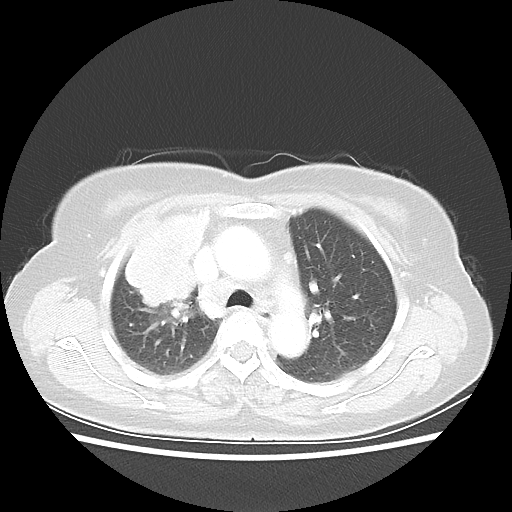
Chest CT, one axial slice; position 37 of 55 along the scan axis; 80 kVp; lung window (W 1500 / L -600 HU); 5 mm slice thickness; 512 × 512 image matrix. Patient: female, 62 years. From the clinical record (not read from this slice): clinical TNM (as recorded): T4 N3 M0.
Structures marked on this image (rectangle marked by the reading radiologist):
- lung tumour (recorded histology: squamous cell carcinoma): bounding box <118,207,212,326> (left, top, right, bottom; pixels)